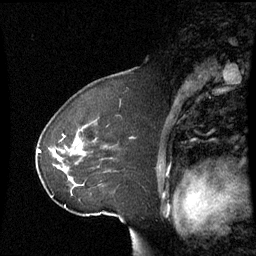
Breast MRI (dynamic contrast-enhanced), one sagittal slice; position 42 of 60 along the scan axis; dynamic contrast-enhanced series, image 2 of 3 at this slice position (ordered by acquisition); 1.5 T; TE 4.2 ms, TR 8.9 ms; 2.4 mm slice thickness; 256 × 256 image matrix. Patient: female, 51 years. Case-level facts recorded for this patient, not image findings: setting: breast cancer imaged before/during neoadjuvant chemotherapy; receptor status: HR-positive, HER2-negative.
Outlined on this slice (semi-automatic segmentation, software-assisted and operator-edited):
- analysis volume of interest (the breast-tissue region the enhancement analysis was run in; not a lesion): bounding box (x1, y1, x2, y2) in pixels: (42, 125, 96, 197)
- tumour enhancement mask (voxels above the 70 % enhancement threshold inside the analysis volume of interest): (74, 141, 77, 145)